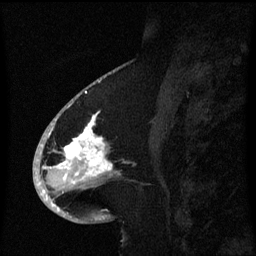
Breast MRI (dynamic contrast-enhanced), one sagittal slice; slice 30 of 60 in the series (ordered by position); dynamic contrast-enhanced series, image 2 of 3 at this slice position (ordered by acquisition); 1.5 T; TE 4.2 ms, TR 8.4 ms; 256 × 256 image matrix, field of view 200 × 200 mm. Patient: female, 53 years. From the clinical record (not read from this slice): setting: breast cancer imaged before/during neoadjuvant chemotherapy; receptor status: HR-positive, HER2-negative.
Outlined on this slice (semi-automatically segmented with operator editing):
- analysis volume of interest (the breast-tissue region the enhancement analysis was run in; not a lesion): bounding box <49,108,120,201> (left, top, right, bottom; pixels)
- tumour enhancement mask (voxels above the 70 % enhancement threshold inside the analysis volume of interest): <57,116,113,177>